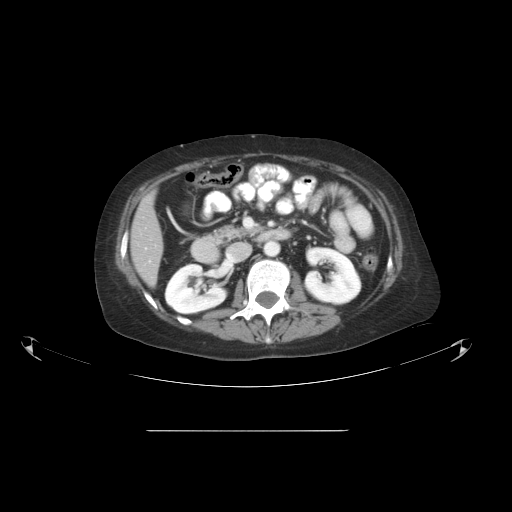
Contrast-enhanced abdominal CT, one axial slice; reconstruction kernel STANDARD; 120 kVp; intravenous contrast given; soft-tissue window (W 400 / L 40 HU); 5 mm slice thickness; 512 × 512 image matrix, field of view 475 × 475 mm. Female patient, age 48 years. Case-level facts recorded for this patient, not image findings: diagnosis: colorectal cancer liver metastases, imaged before liver resection; multiple liver metastases: yes; largest metastasis: 1 cm; disease in both lobes: no.
Outlined on this slice (outlined manually by an expert reader):
- liver: bounding box <132,195,164,286> (left, top, right, bottom; pixels)
- planned liver remnant (the part of the liver to remain after resection): <132,195,164,286>